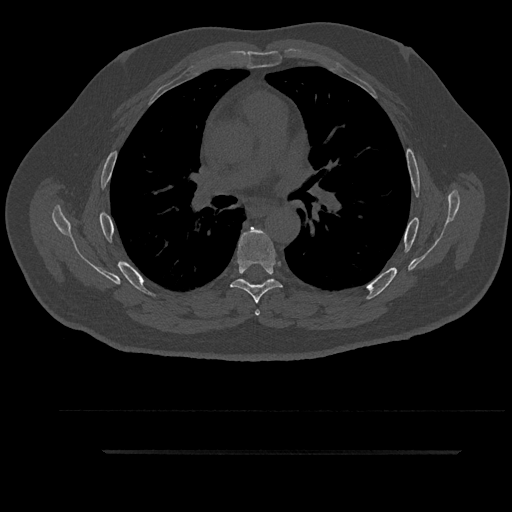
CT including the spine, one axial slice; position 581 of 797 along the scan axis; reconstruction kernel Br40s/3; bone window (W 1800 / L 400 HU); 0.5 mm slice thickness; 512 × 512 image matrix, field of view 432 × 432 mm. Patient: male, 63 years. From the clinical record (not read from this slice): primary cancer: renal.
Structures marked on this image (semi-automatic segmentation, software-assisted and operator-edited):
- T5 vertebra: bounding box <244,227,266,316> (left, top, right, bottom; pixels)
- T6 vertebra: <230,227,282,304>